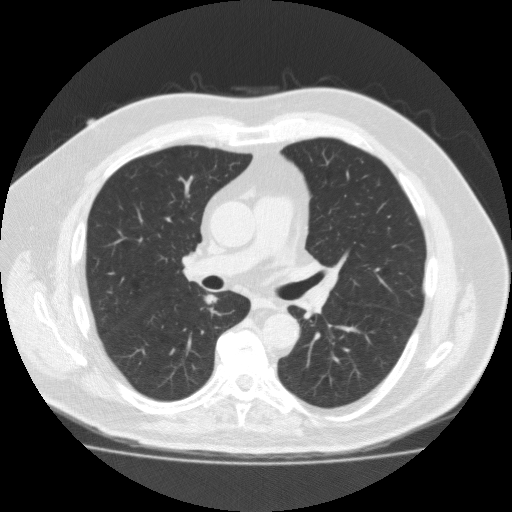
Axial slice from a low-dose chest CT screening exam; third screening round (two years after baseline); lung window (W 1500 / L -600 HU); 120 kVp. Male, age 56 years at enrolment. Current smoker at enrolment.
Expert-annotated lung lesion, bounding box (x1, y1, x2, y2) in pixels: (187, 281, 230, 317). Screening reader's record for this exam (one nodule recorded; not confirmed to be the boxed lesion): non-calcified nodule or mass ≥4 mm, right lower lobe, 12 × 8 mm, spiculated (stellate) margins, soft tissue attenuation, pre-existing on the prior screen: yes; interval growth: yes. Later outcome: lung cancer diagnosed 49 days after this screen — adenocarcinoma, NOS, right lower lobe, moderately differentiated (G2), stage IA (AJCC 6th edition), 12 mm at pathology.